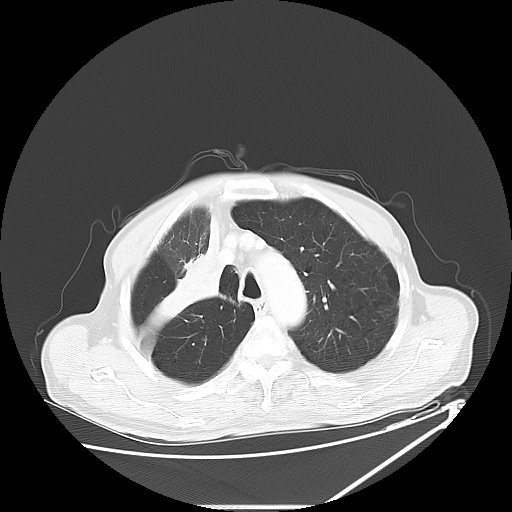
Chest CT, one axial slice; position 48 of 60 along the scan axis; reconstruction kernel LUNG; lung window (W 1500 / L -600 HU); 5 mm slice thickness; 512 × 512 image matrix, field of view 410 × 410 mm. Patient: male, 73 years. From the clinical record (not read from this slice): clinical TNM (as recorded): T2a N1 M0.
Outlined on this slice (rectangle marked by the reading radiologist):
- lung tumour (recorded histology: squamous cell carcinoma): bounding box (x1, y1, x2, y2) in pixels: (139, 218, 242, 350)